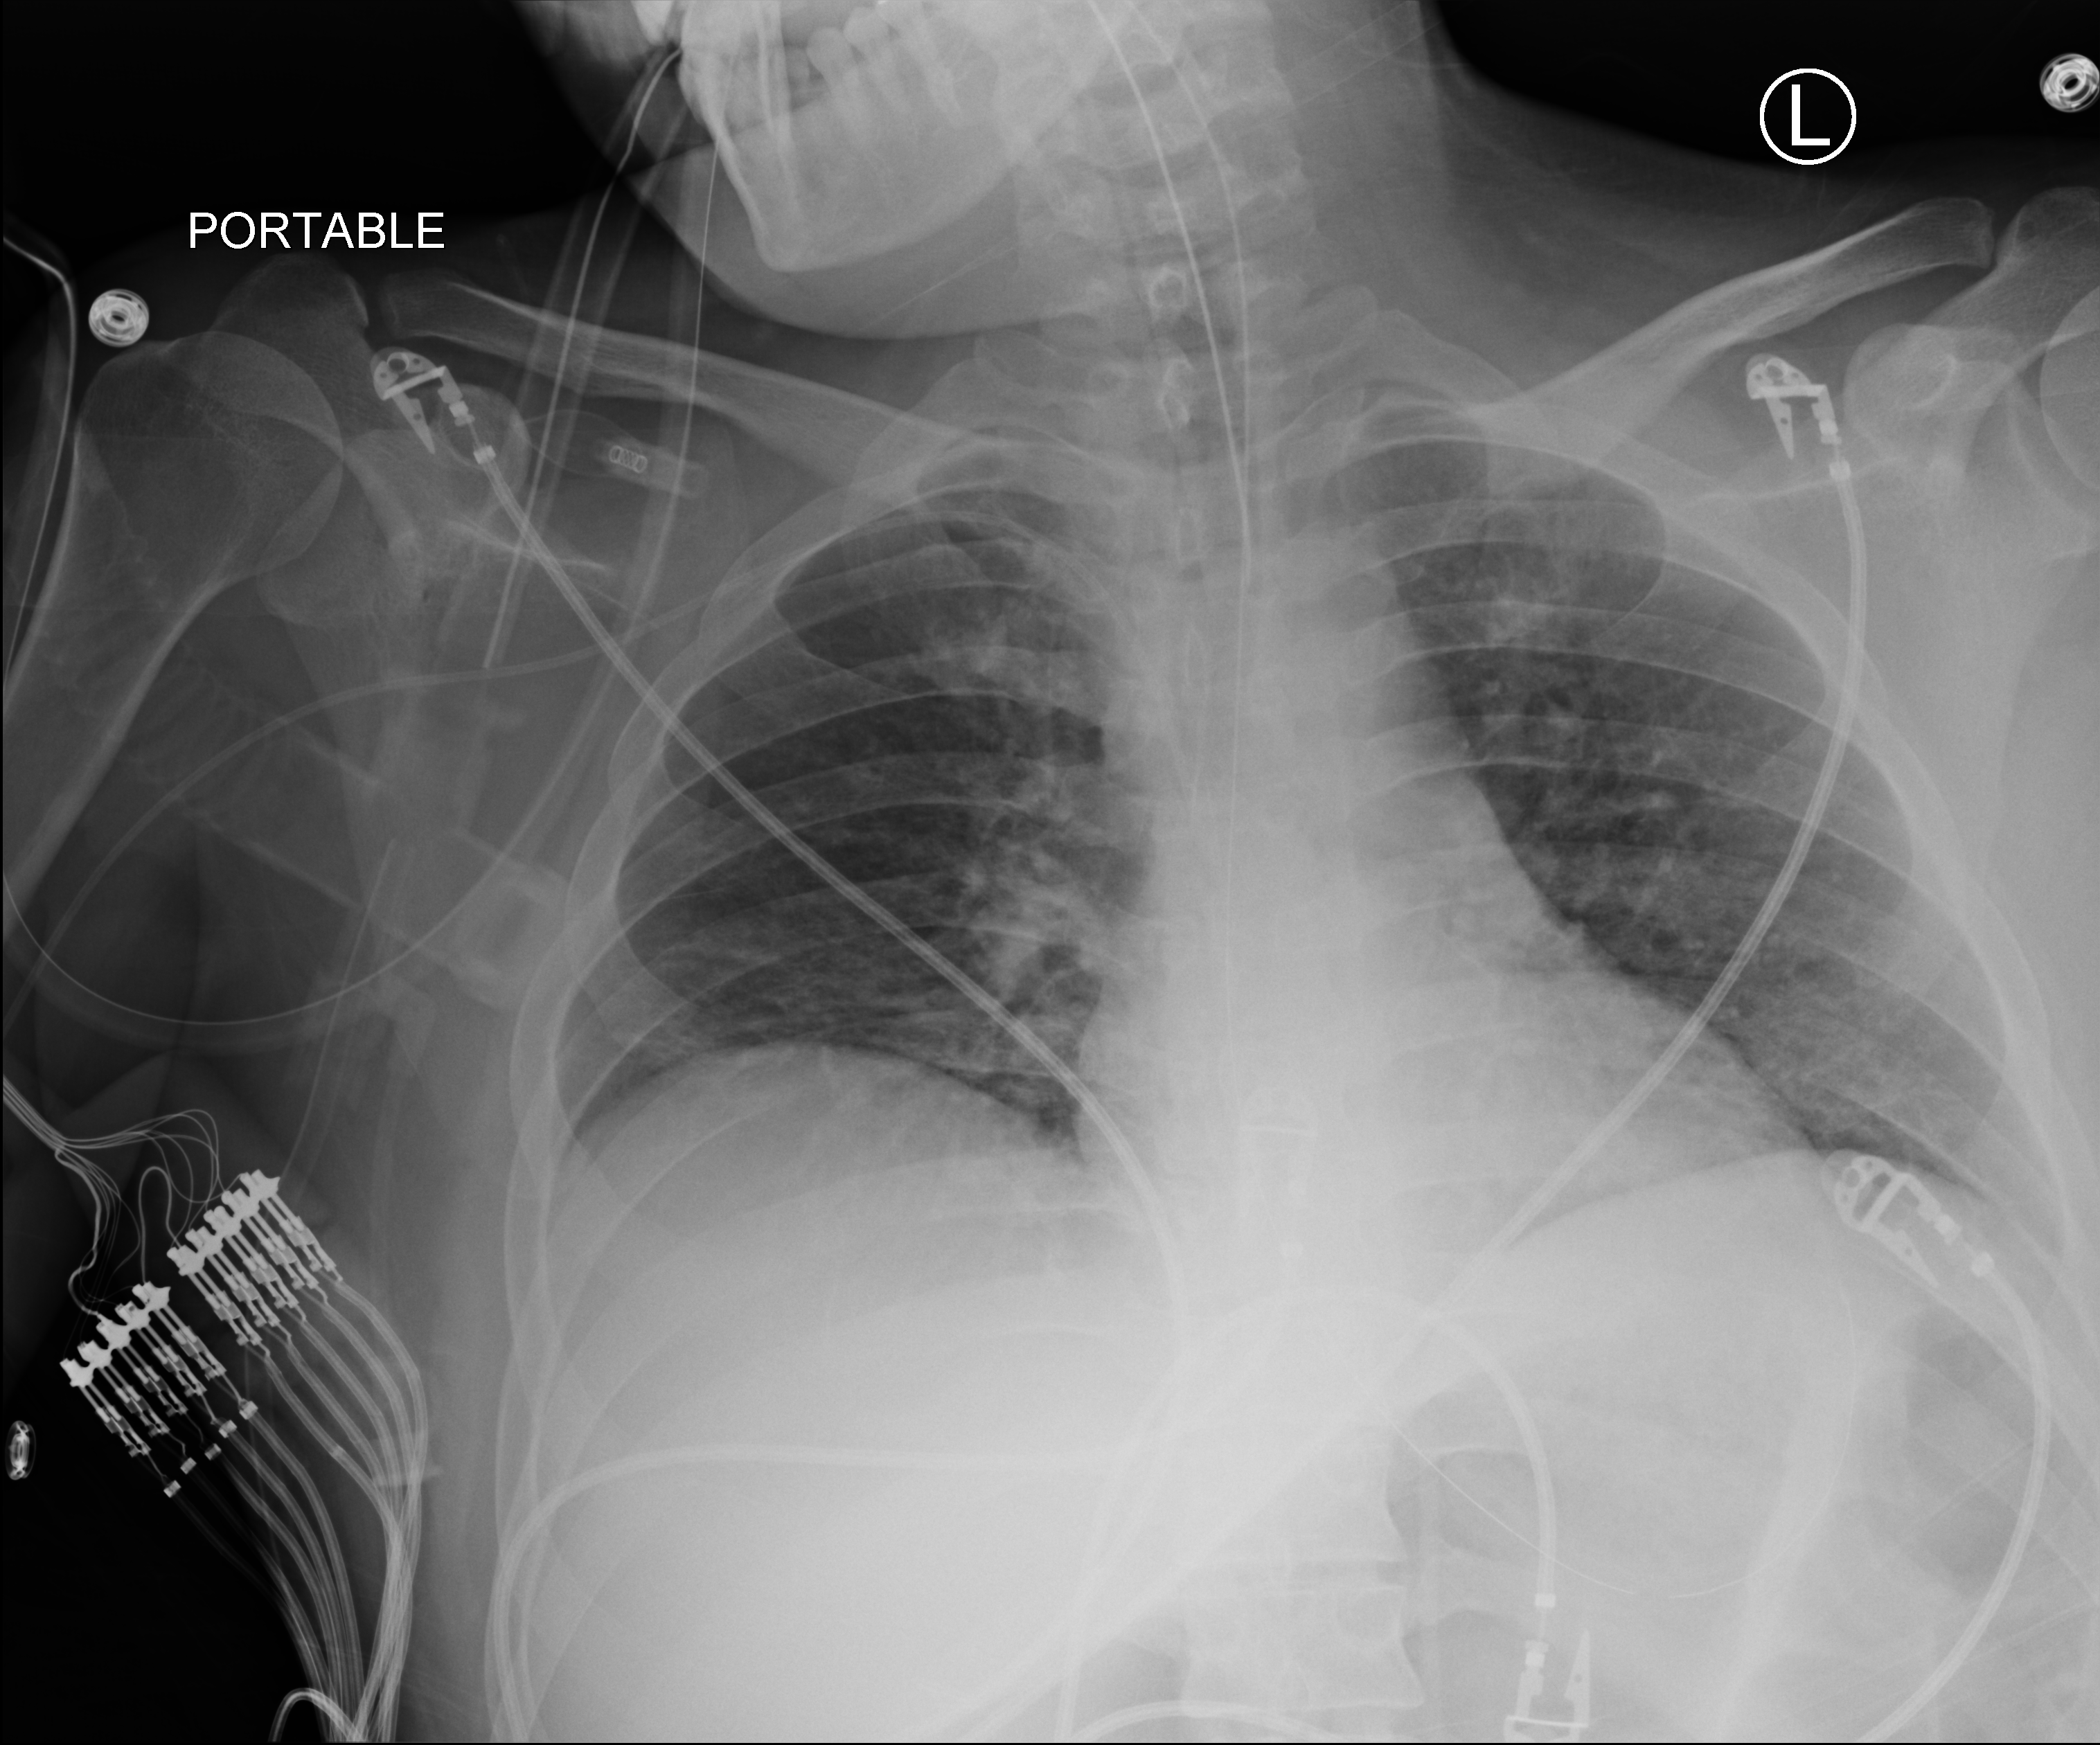
Chest X-ray (portable), anteroposterior (AP) projection. Male patient hospitalised with COVID-19, age 18–59 years.
From the hospital-stay record, not from the radiograph (when in the stay this image was taken is not recorded): admitted to intensive care during this hospital stay: yes; mechanically ventilated during this hospital stay: yes.